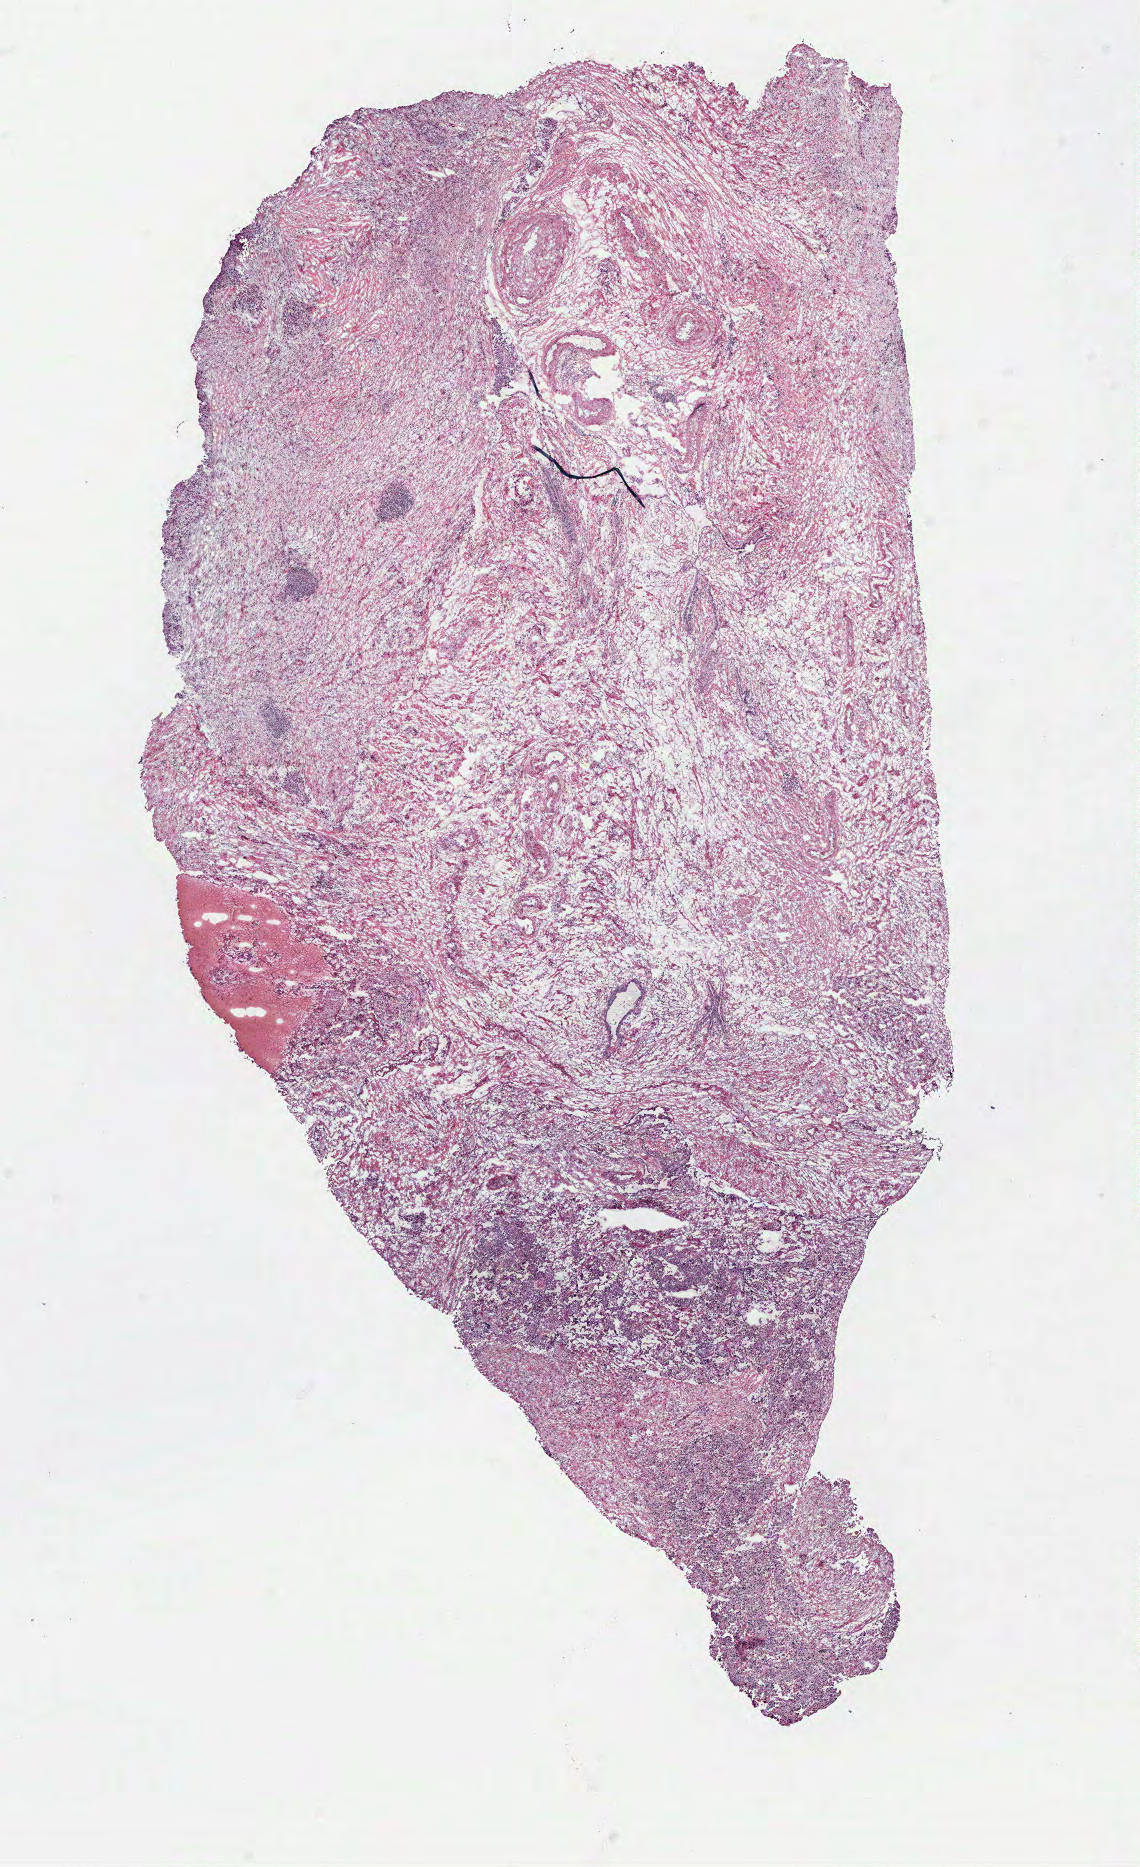
Whole-slide histology image, H&E-stained — low-resolution overview of the scanned area, about 9.1 x 14.9 mm (from a 40x scan), normal (non-tumour) tissue sample, ovary. Female, 65 y/o.
This section: normal (non-tumour) tissue from the same patient. Patient diagnosis (cohort enrolment): ovarian cancer (ovary).